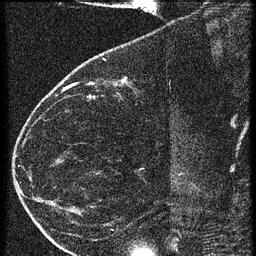
Breast MRI (dynamic contrast-enhanced), one sagittal slice. Position 19 of 60 along the scan axis. 3 images stored at this slice position (order not interpretable as contrast timing). 1.5 T. TE 4.2 ms, TR 20.4 ms. 1.5 mm slice thickness. 256 × 256 image matrix, field of view 180 × 180 mm. Female patient, age 35 years. Case-level facts recorded for this patient, not image findings: setting: breast cancer imaged before/during neoadjuvant chemotherapy; receptor status: HR-positive, HER2-negative.
Structures marked on this image (semi-automatic segmentation, software-assisted and operator-edited):
- analysis volume of interest (the breast-tissue region the enhancement analysis was run in; not a lesion): box from (x=65, y=60) to (x=169, y=119) px
- tumour enhancement mask (voxels above the 90 % enhancement threshold inside the analysis volume of interest): (x=122, y=80)–(x=125, y=83)